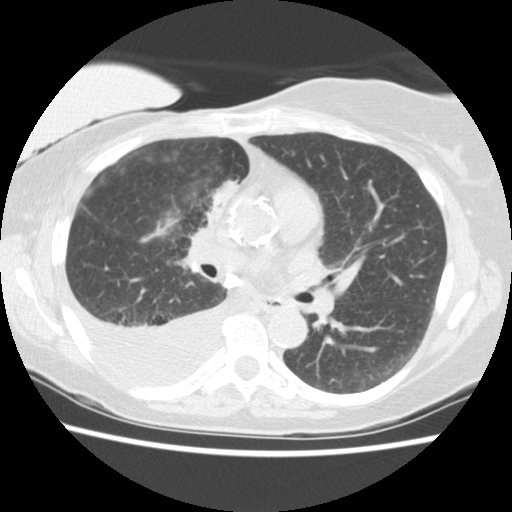
Low-dose screening chest CT, one axial slice. Slice 83 of 157 in the series (ordered by position). Reconstruction kernel STANDARD. Lung window (W 1500 / L -600 HU). 2.5 mm slice thickness. 512 × 512 image matrix.
Structures marked on this image (manually delineated by an expert):
- lesion 1 (tumor, upper lobe of right lung): bounding box (x1, y1, x2, y2) in pixels: (210, 180, 240, 216)